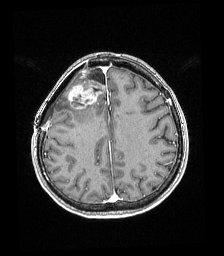
Brain MRI from a brain-tumour surgery series, one axial slice; position 65 of 192 along the scan axis; T1-weighted post-contrast; 1 mm slice thickness; 224 × 256 image matrix, field of view 219 × 250 mm. From the clinical record (not read from this slice): histopathology: Astrocytoma; WHO grade: 4; IDH mutation: yes; tumour location: Right superficial frontal.
Structures marked on this image (expert manual segmentation):
- tumour: bounding box (x1, y1, x2, y2) in pixels: (67, 68, 100, 109)